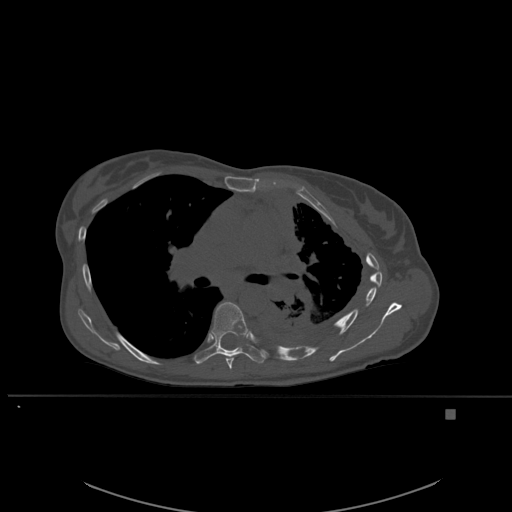
CT including the spine, one axial slice. Slice 371 of 537 in the series (ordered by position). Bone window (W 1800 / L 400 HU). 512 × 512 image matrix, field of view 440 × 440 mm. Patient: female, 45 years. Case-level facts recorded for this patient, not image findings: primary cancer: lung.
Outlined on this slice (semi-automatically segmented with operator editing):
- T6 vertebra: bounding box [x1, y1, x2, y2] px = [225, 357, 234, 370]
- T7 vertebra: [196, 302, 266, 364]